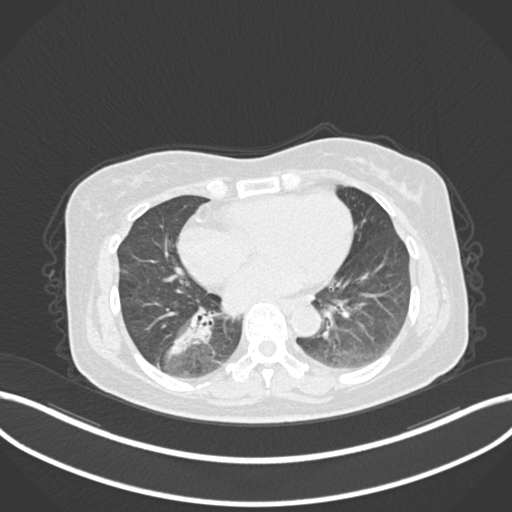
Chest CT, one axial slice. Lung window (W 1500 / L -600 HU). 512 × 512 image matrix, field of view 400 × 400 mm. Patient: female, 67 years. From the clinical record (not read from this slice): clinical TNM (as recorded): T1c N1 M0; histopathological grade: G2-3.
Outlined on this slice (bounding box drawn by a radiologist):
- lung tumour (recorded histology: adenocarcinoma): bounding box <158,301,228,364> (left, top, right, bottom; pixels)